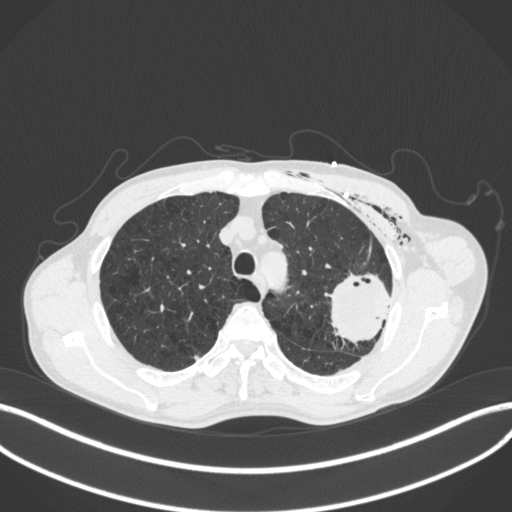
Chest CT, one axial slice; position 314 of 416 along the scan axis; 120 kVp; lung window (W 1500 / L -600 HU); 1 mm slice thickness; 512 × 512 image matrix. Patient: male, 58 years. From the clinical record (not read from this slice): clinical TNM (as recorded): T3 N0 M0.
Structures marked on this image (rectangle marked by the reading radiologist):
- lung tumour (recorded histology: adenocarcinoma): bounding box (x1, y1, x2, y2) in pixels: (324, 270, 398, 346)